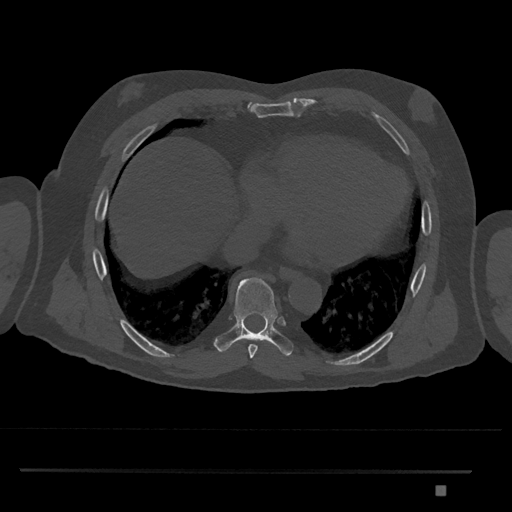
CT including the spine, one axial slice. Reconstruction kernel Br40s/3. 120 kVp. Bone window (W 1800 / L 400 HU). 512 × 512 image matrix, field of view 429 × 429 mm. Patient: male, 65 years. Case-level facts recorded for this patient, not image findings: primary cancer: prostate.
Annotated regions visible in this slice (semi-automatically segmented with operator editing):
- T8 vertebra: bounding box <213,275,294,356> (left, top, right, bottom; pixels)